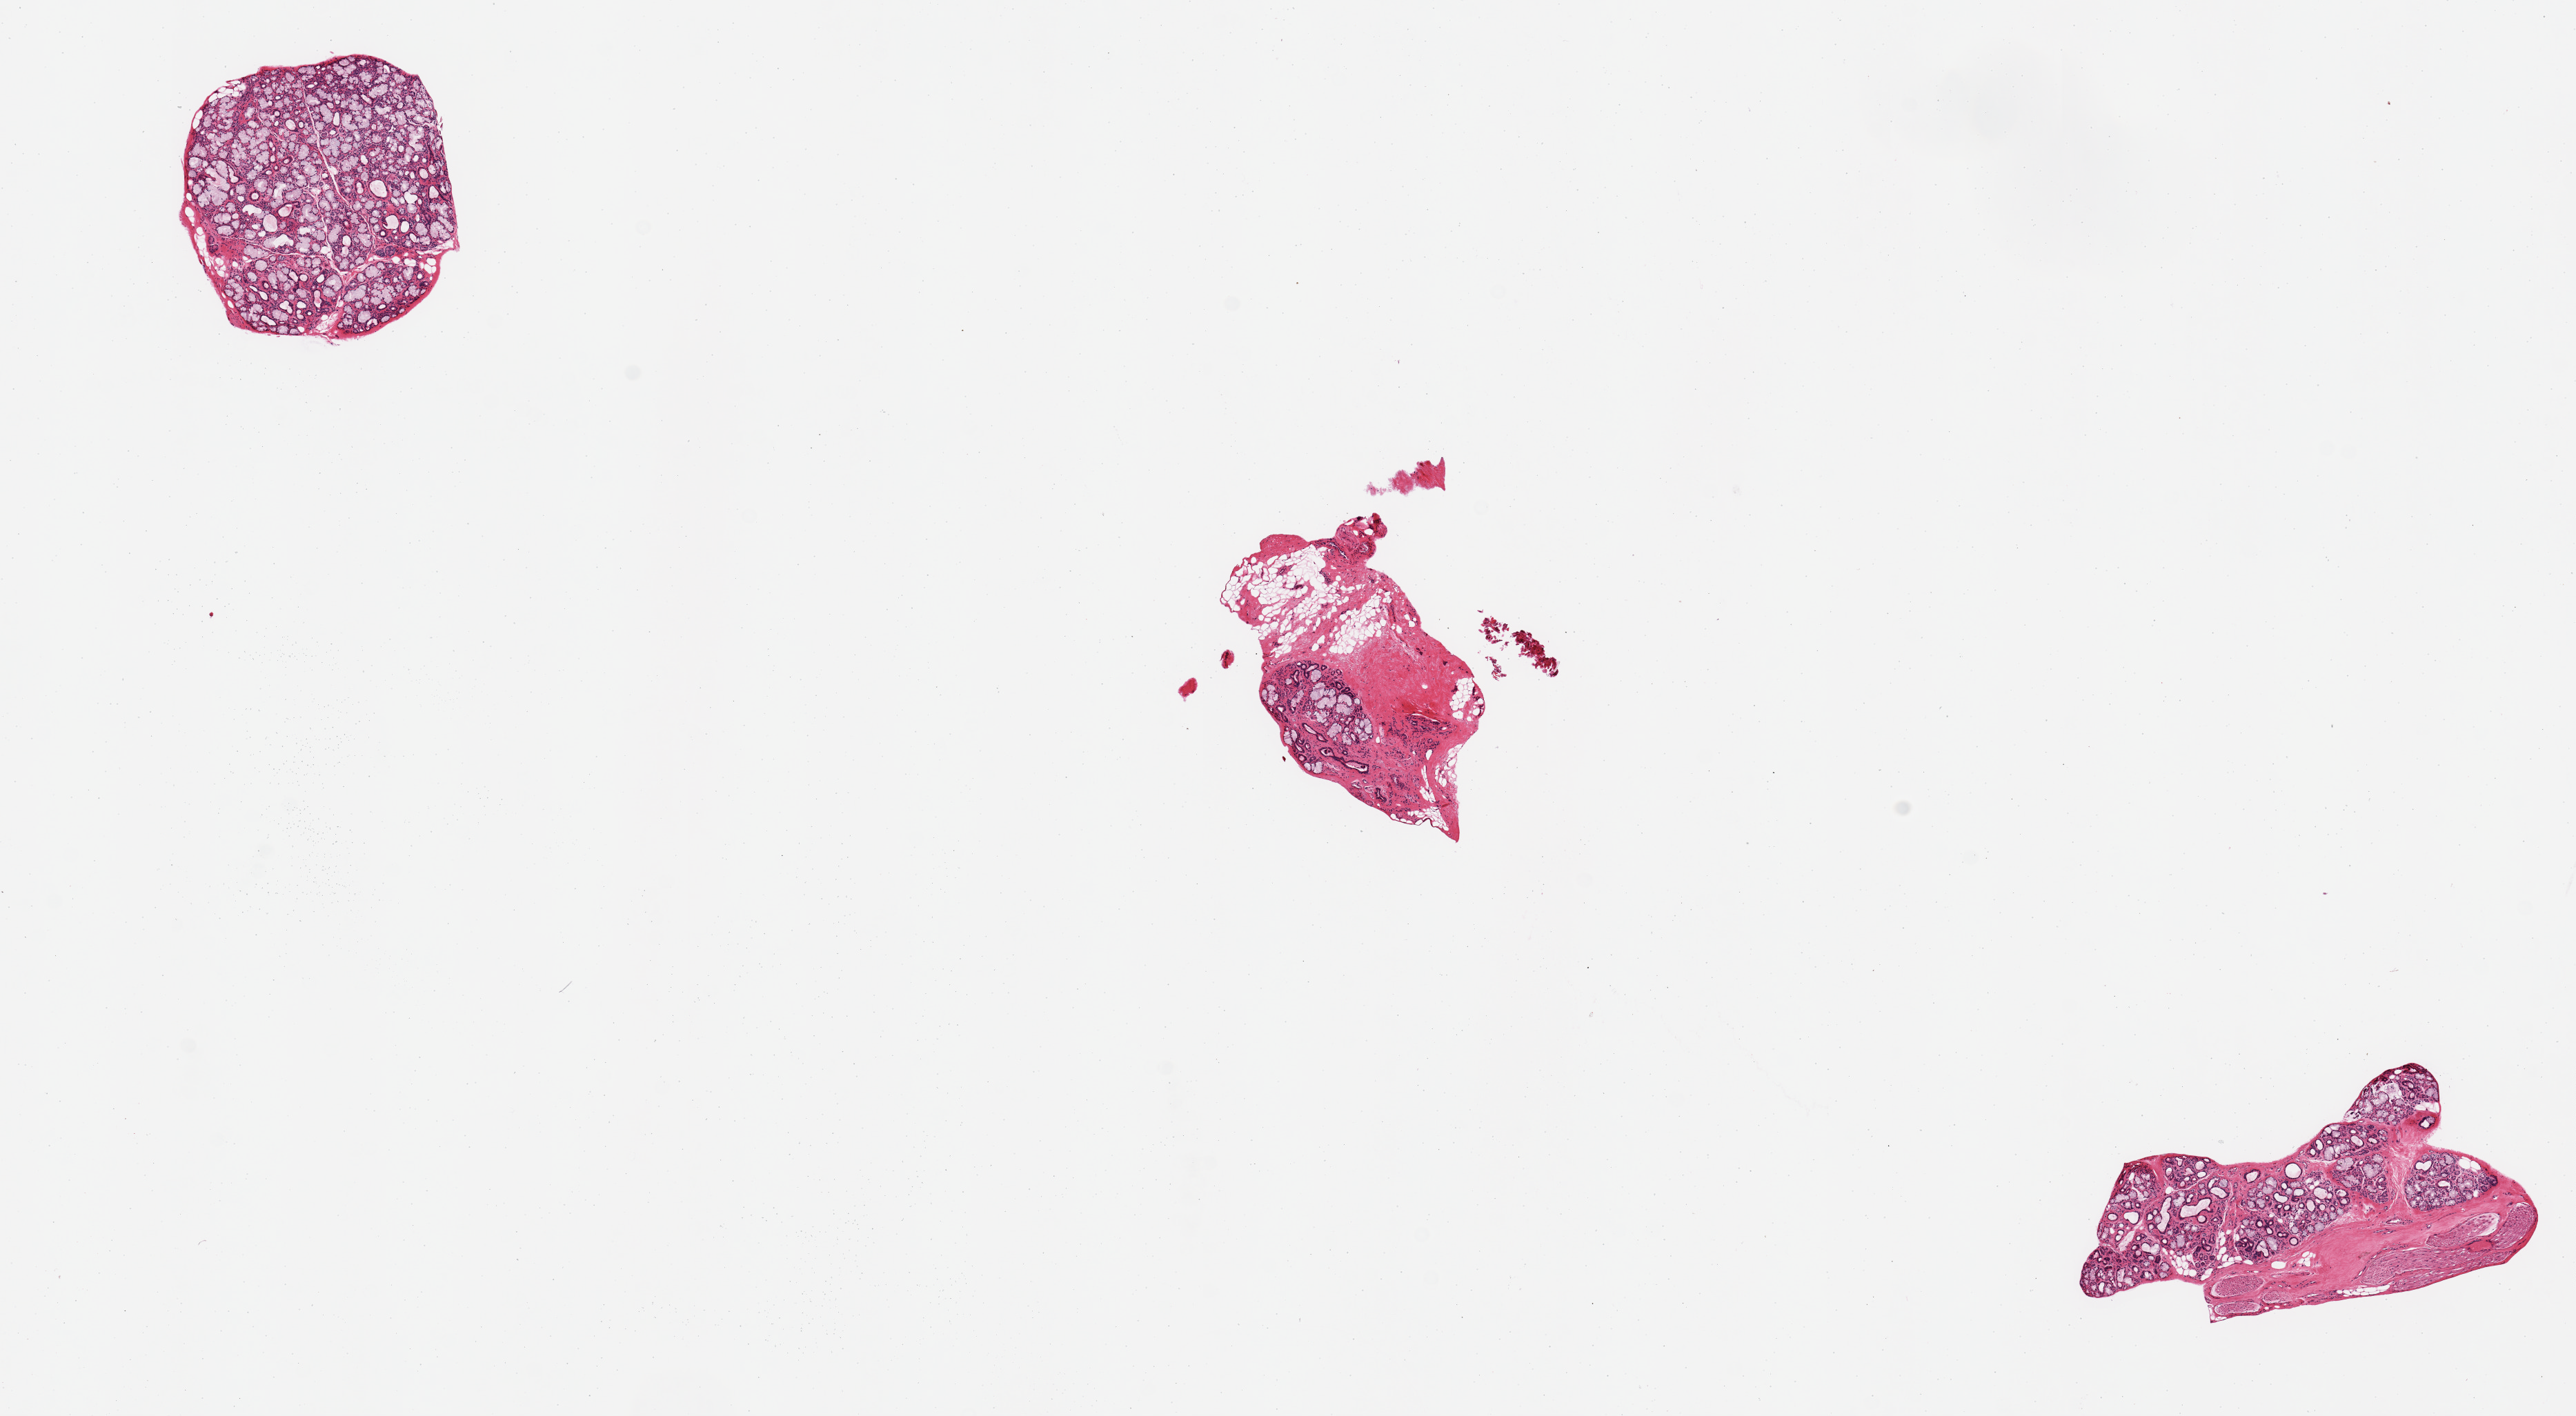
Hematoxylin and eosin (H&E) whole-slide image — a low-resolution overview of the entire scanned area, about 14.8 x 8.1 mm; PAXgene-fixed paraffin-embedded (PFPE) section; sampled site (target tissue): minor salivary gland; donor tissue sample. Donor sex: male.
* review note (as recorded): 3 pieces; 1 robust gland, 2 atrophic with fibrofatty stroma & nerves